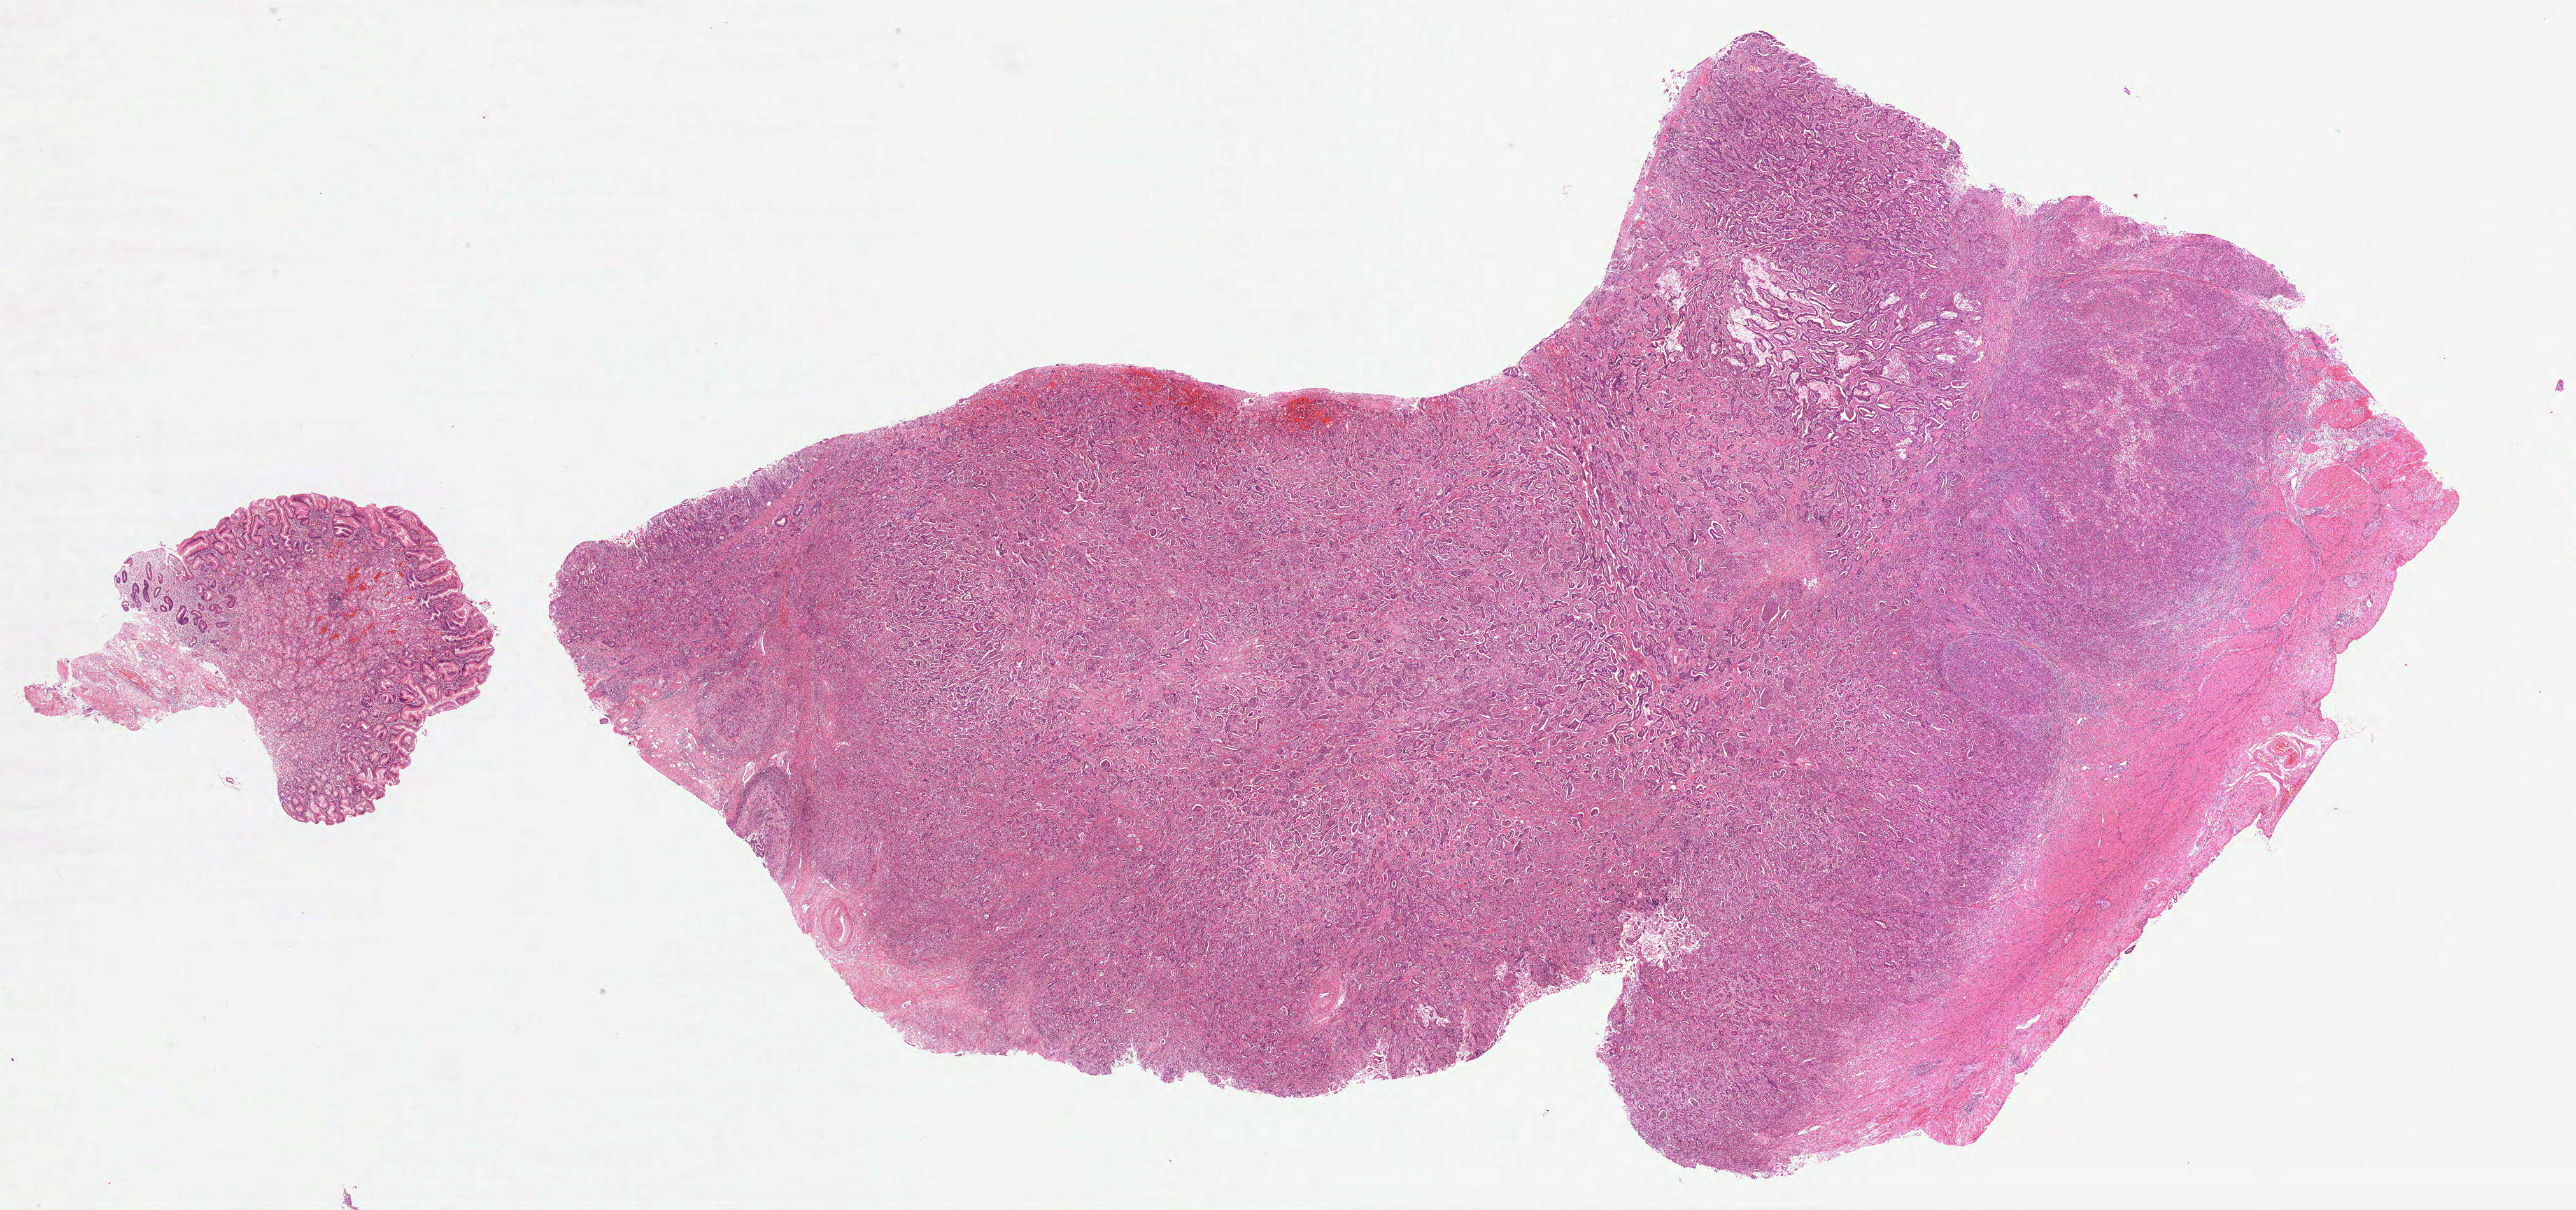
Whole-slide histology image, H&E — low-resolution overview of the scanned area, about 32.6 x 15.3 mm (acquisition: 40x scan). Formalin-fixed paraffin-embedded (FFPE) diagnostic section. Sample: primary tumour, stomach. Female patient; age at initial diagnosis 67 years. Histologic grade: G3 (poorly differentiated).
* histologic diagnosis: Adenocarcinoma, NOS (gastric antrum)
* AJCC pathologic stage: IIIC (7th edition)